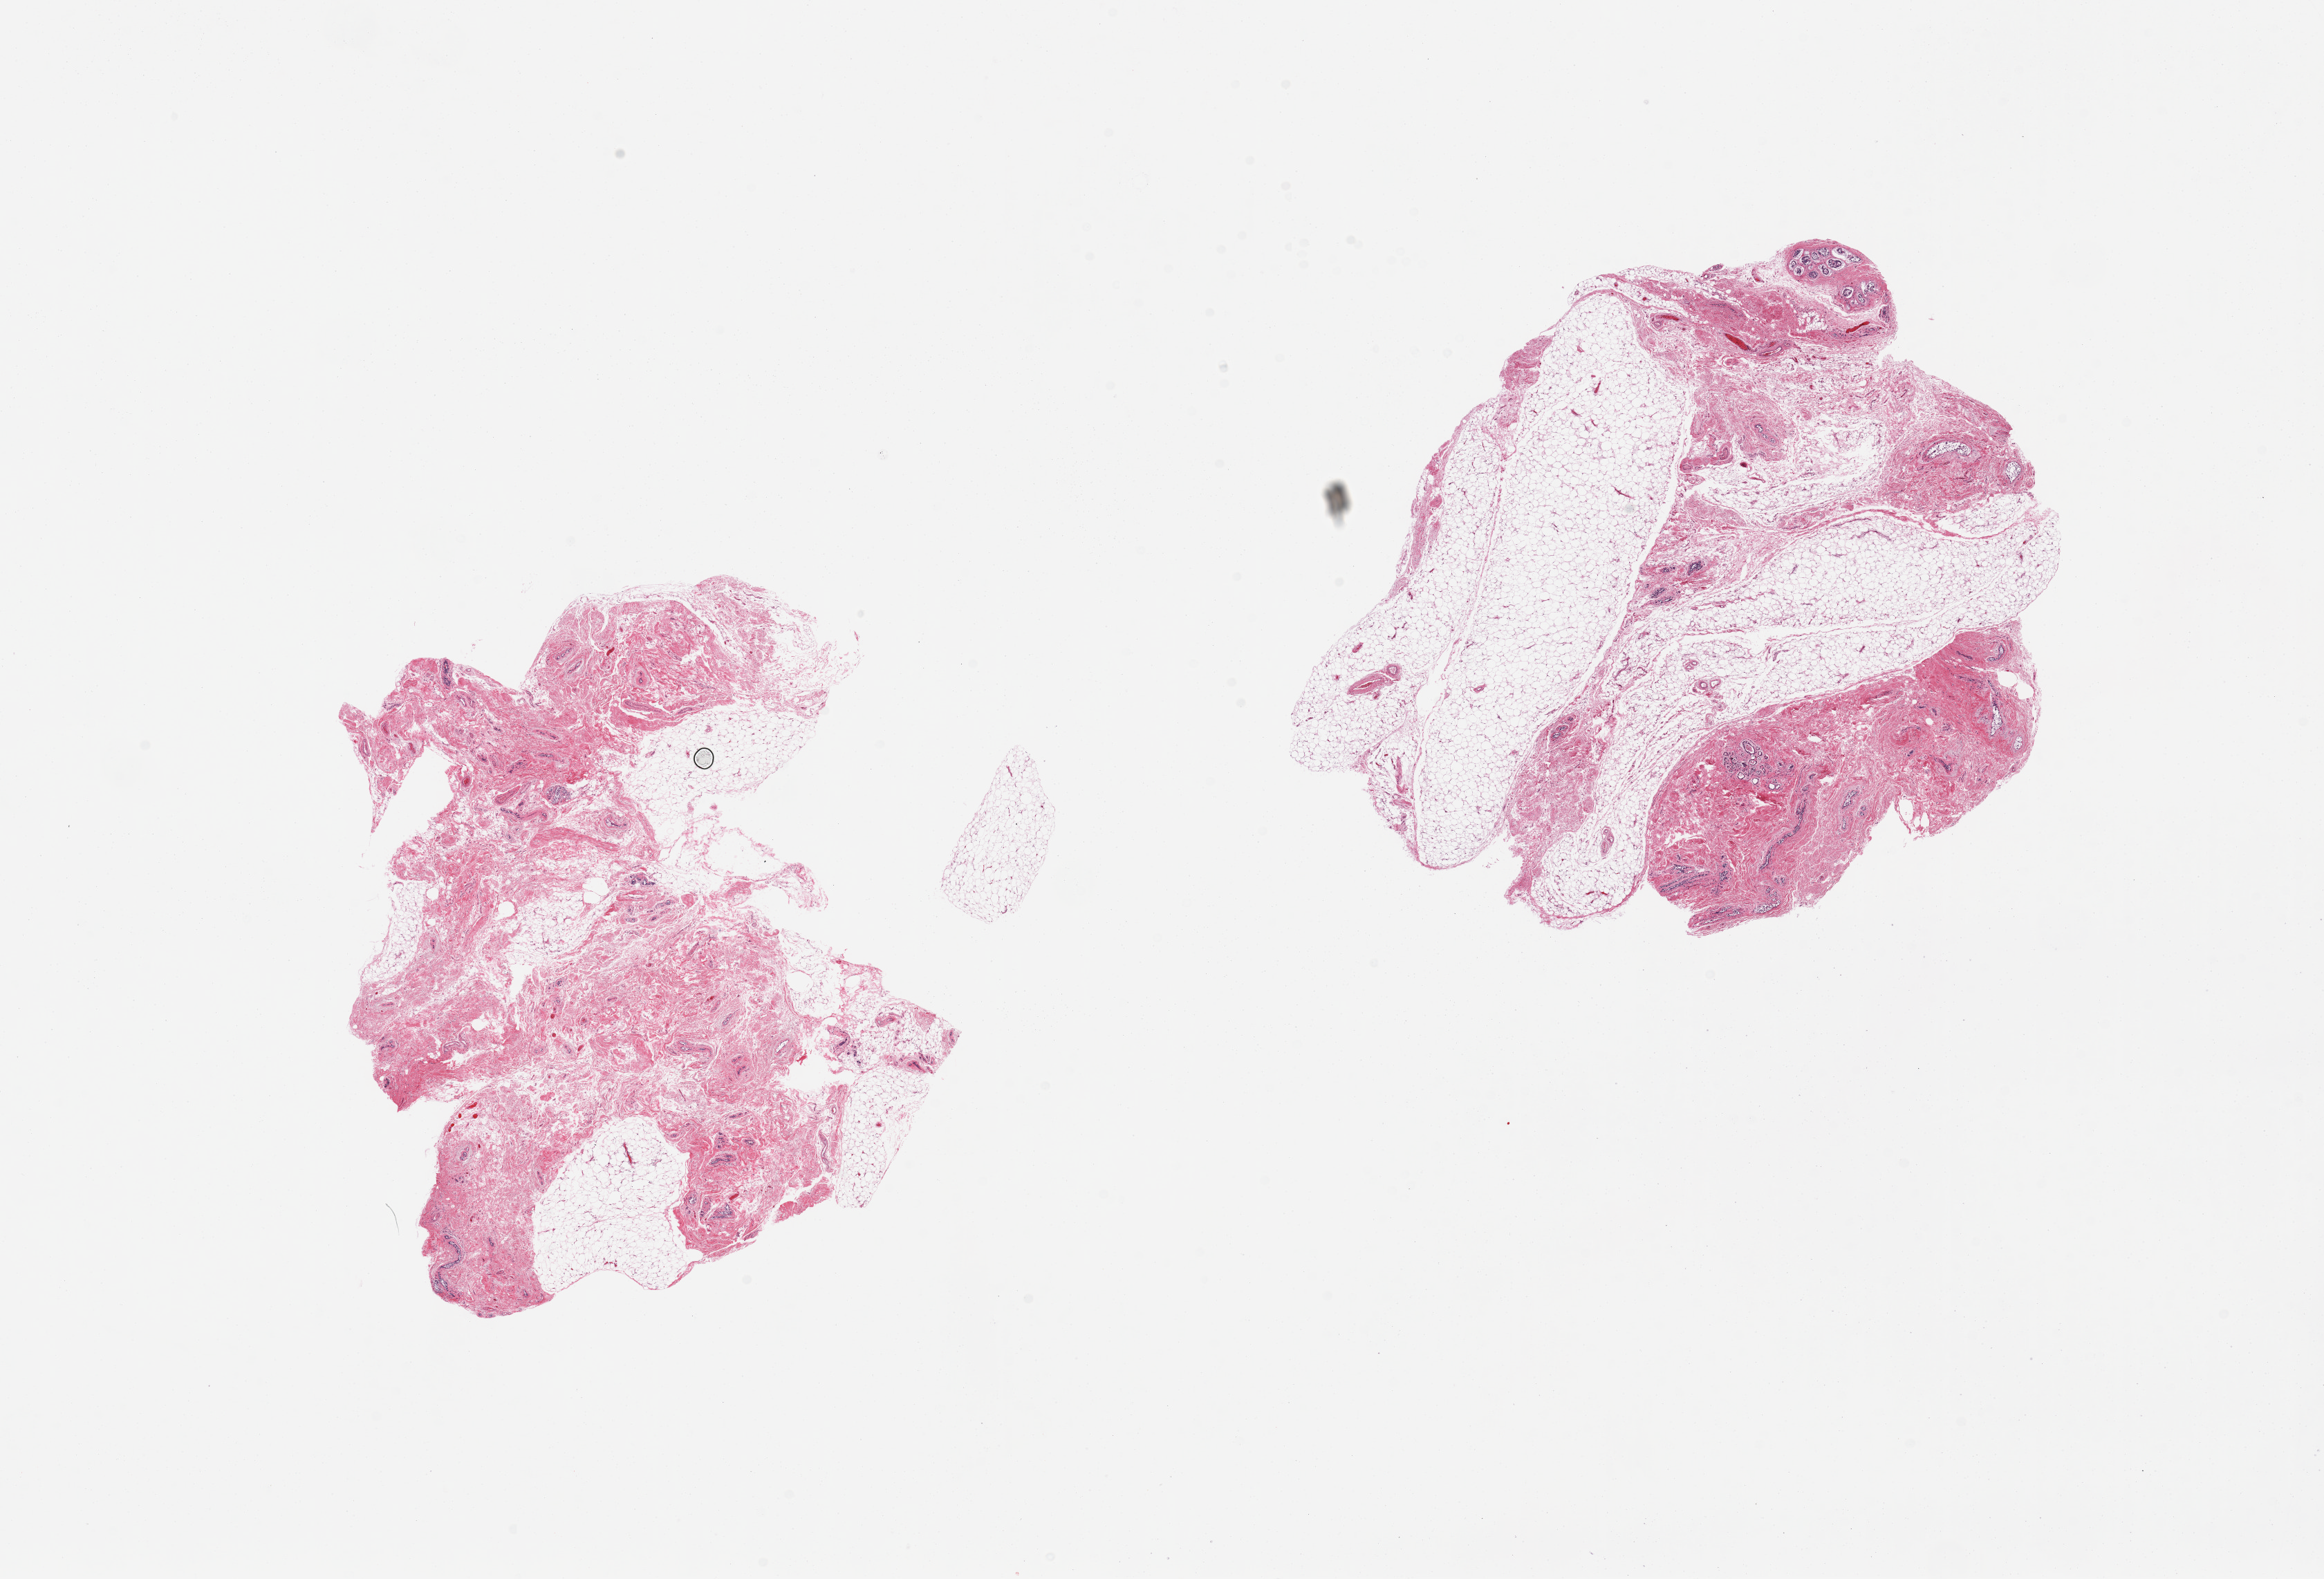
Whole-slide image, hematoxylin and eosin (H&E) stain, brightfield — low-resolution overview of the scanned area, about 26.6 x 18.1 mm, PAXgene-fixed paraffin-embedded (PFPE) section, section of breast (target tissue), donor tissue sample. Donor sex: female.
- reviewer comment on this tissue sample: 2 pieces; atrophic ducts& lobules